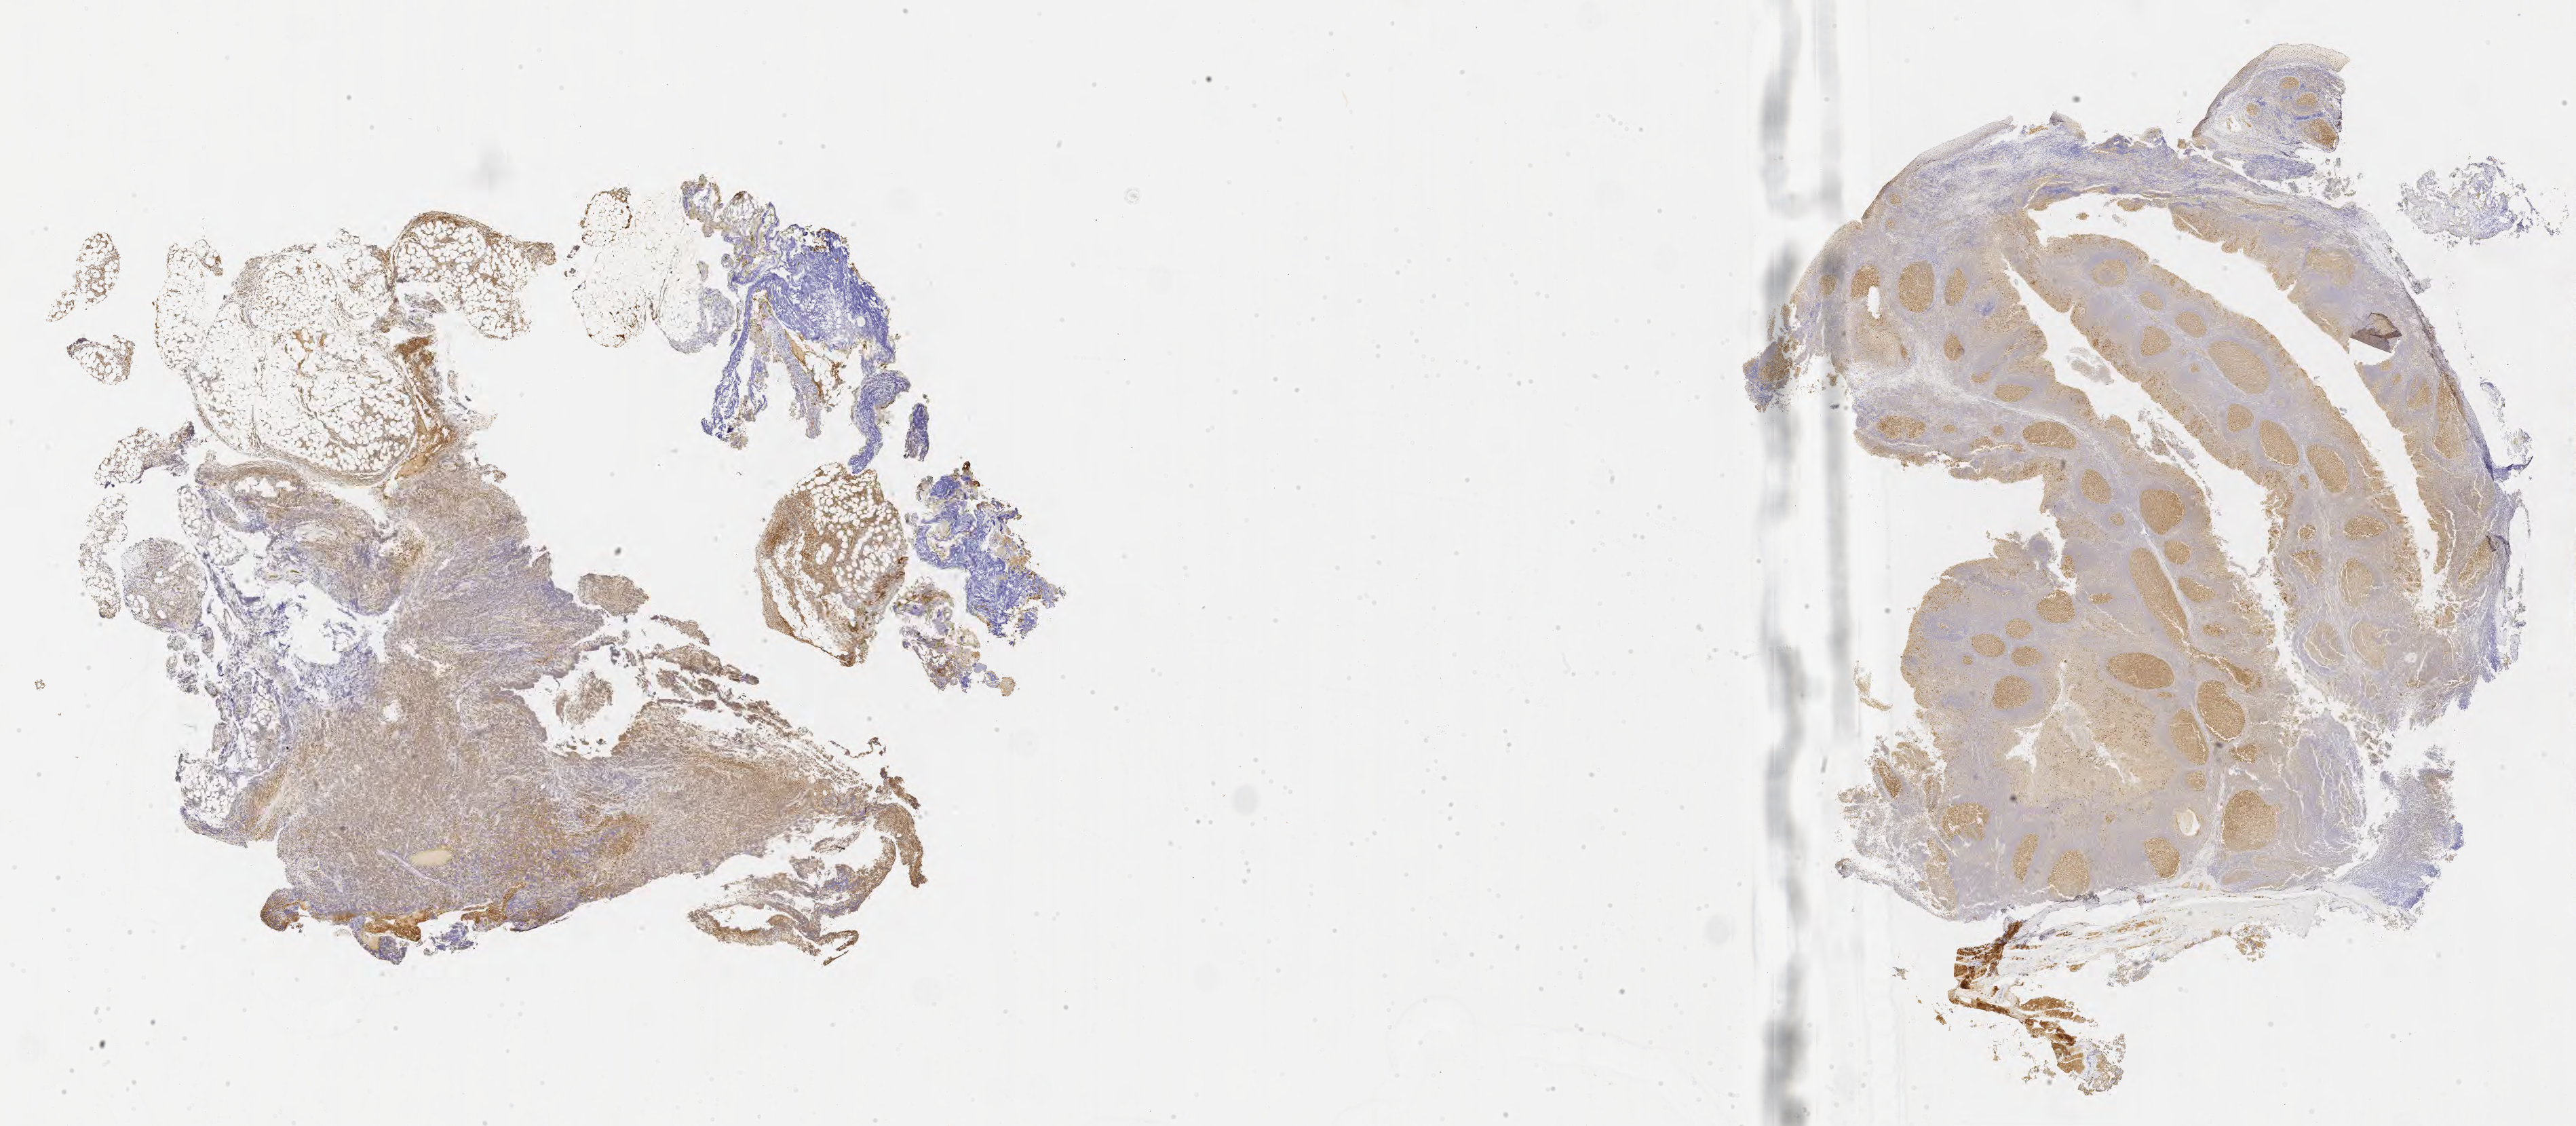
Immunohistochemistry (IHC) whole-slide image stained for BCL6 — shown as a low-resolution overview of the whole scanned area (about 30.7 x 13.4 mm). Tumor tissue. Anatomic site: abdominal lymph node. Male, age 9 years at initial diagnosis.
Histologic diagnosis: Burkitt lymphoma, NOS.